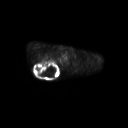
FDG PET of an extremity soft-tissue mass (from a PET/CT study), one axial slice; slice 207 of 267 in the series (ordered by position); 3.27 mm slice thickness; 128 × 128 image matrix, field of view 700 × 700 mm. Male patient, age 61 years. Case-level facts recorded for this patient, not image findings: histological type: pleiomorphic spindle cell undifferentiated; grade: high; site of the primary tumour: right parascapusular.
Annotated regions visible in this slice (expert contour drawn on MRI and transferred to this co-registered scan by the dataset authors):
- gross tumour volume including surrounding oedema: bounding box <33,60,60,77> (left, top, right, bottom; pixels)
- gross tumour volume (mass): <34,61,59,77>